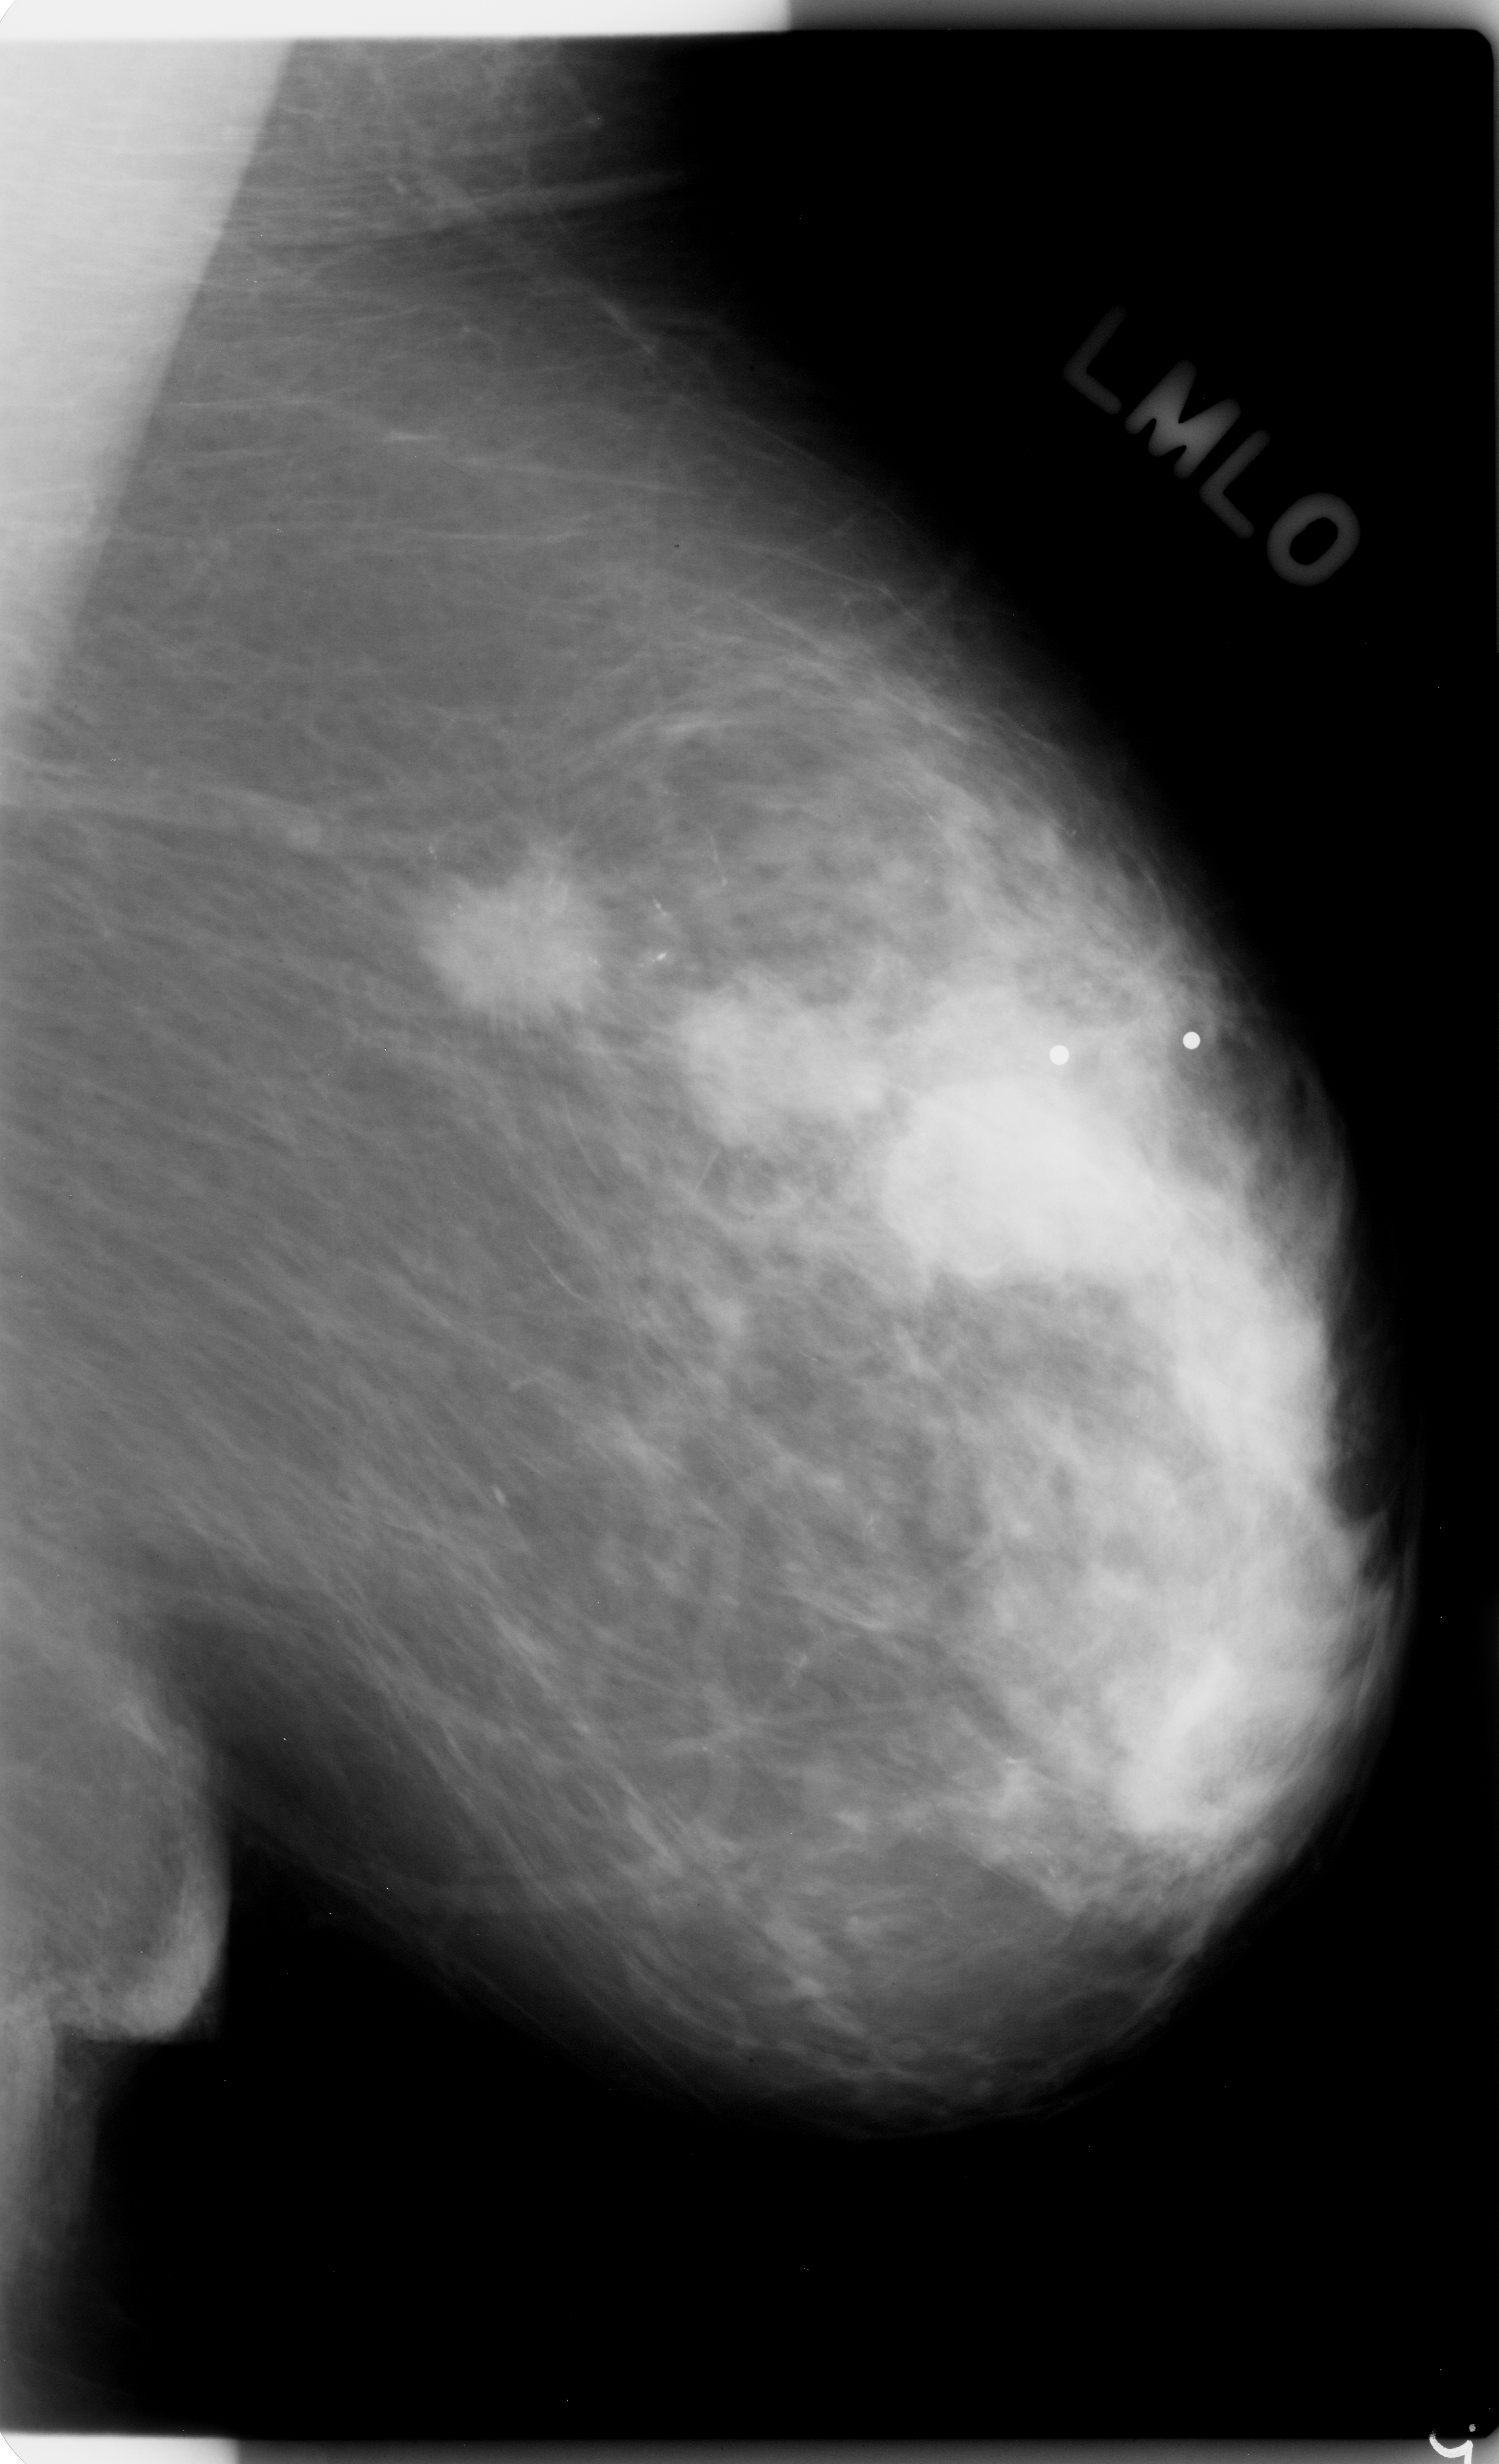
Mammogram (digitized film), left breast, mediolateral oblique (MLO) view, BI-RADS breast density category 2 (scale 1–4).
Marked findings (only marked abnormalities are described; nothing is implied about the rest of the image): Finding 1 of 3: mass, shape irregular, margins spiculated; BI-RADS assessment category 5; pathology result (as recorded, not read from the image): malignant. Finding 2 of 3: mass, shape irregular, margins spiculated; BI-RADS assessment category 5; subtlety rating 5 on a 1 (subtle) to 5 (obvious) scale; pathology (as recorded): malignant. Finding 3 of 3: mass, shape irregular, margins spiculated; BI-RADS assessment category 5; pathology result (as recorded, not read from the image): malignant.